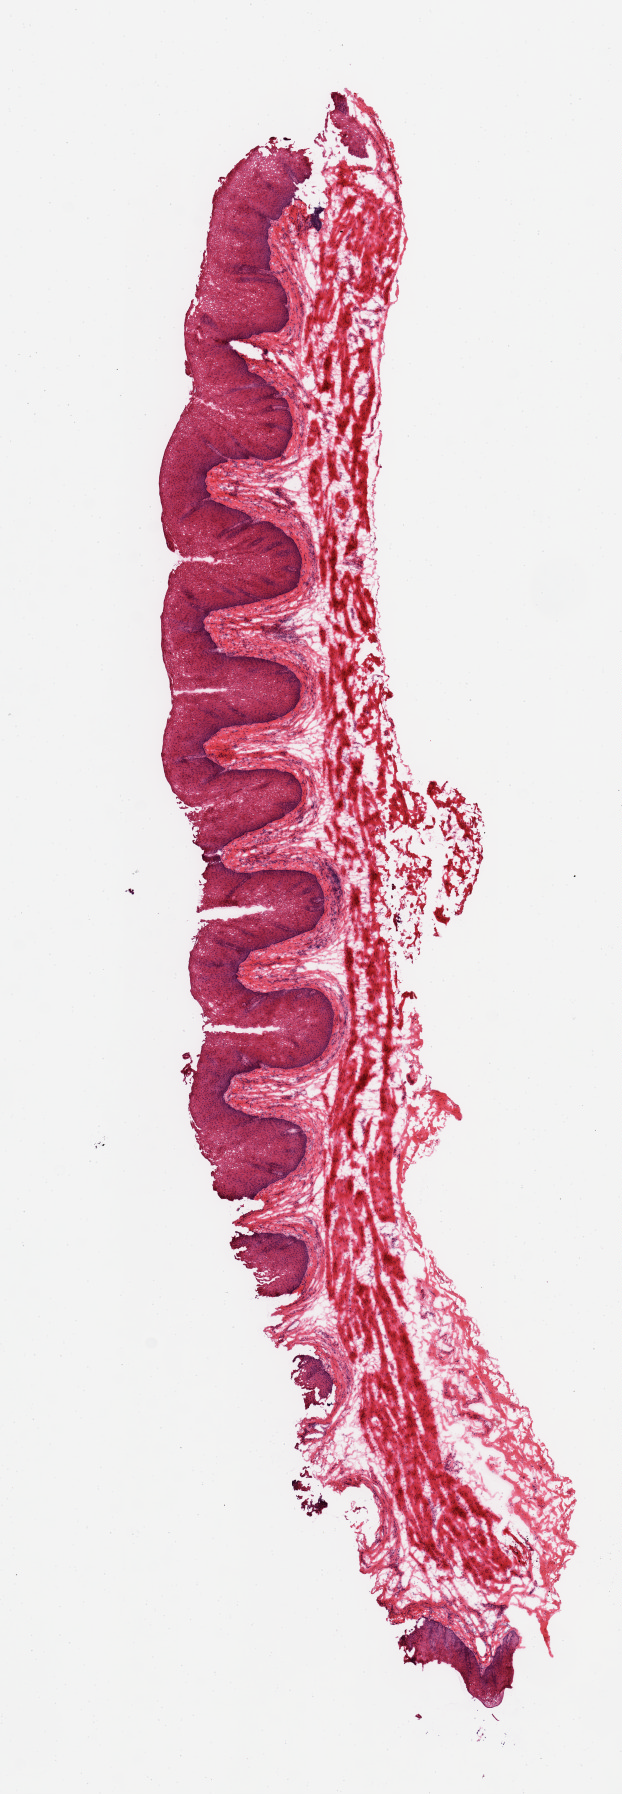
Digitized haematoxylin and eosin-stained section, low-resolution overview of the scanned area, about 4.9 x 14.2 mm (acquisition: 20x scan), frozen section, sampled site (target tissue): esophageal mucous membrane, donor tissue sample. Female donor.
Pathologist's review note for this sample: 1 piece.